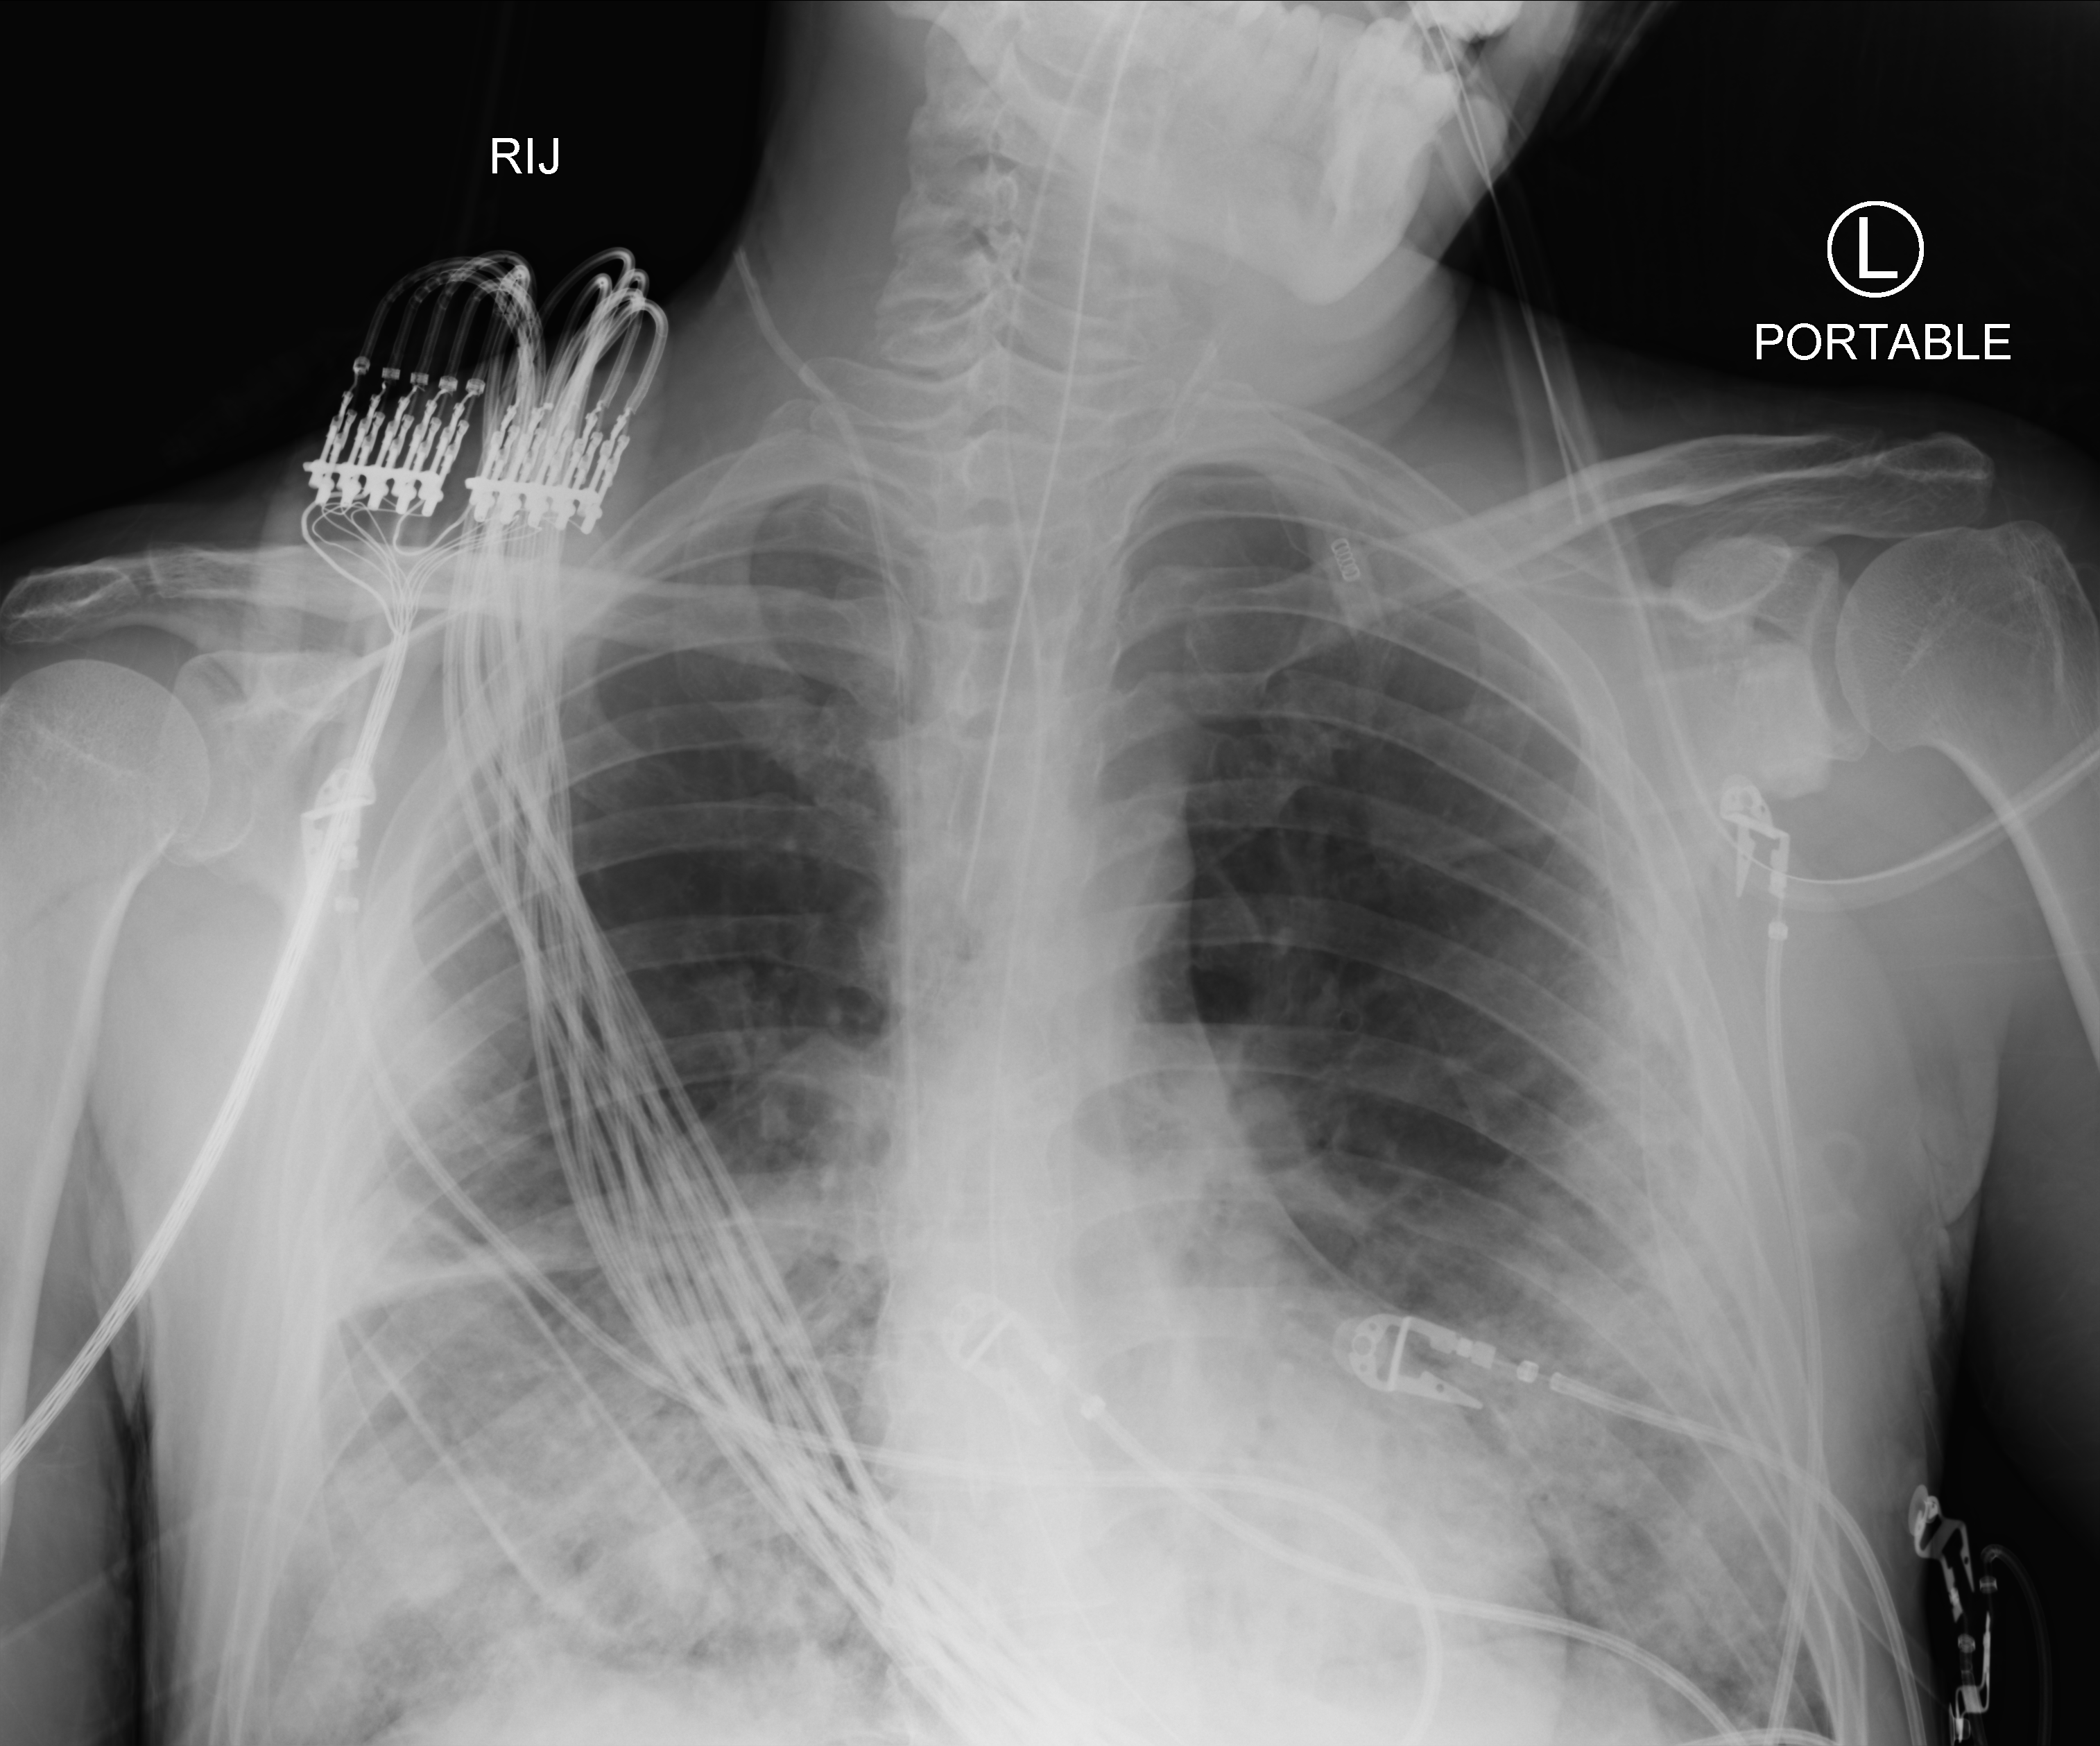
Chest X-ray (portable), anteroposterior (AP) projection. Male patient hospitalised with COVID-19, age 18–59 years.
Hospital-stay facts (about this admission, not read from this image; timing relative to this image not recorded): length of hospital stay: 96 days.